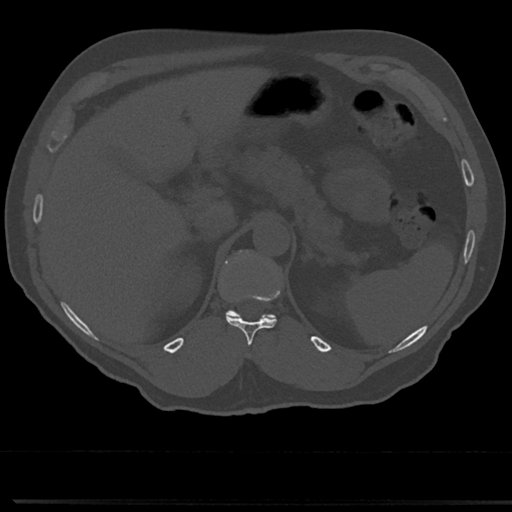
CT including the spine, one axial slice; slice 182 of 817 in the series (ordered by position); reconstruction kernel Br40s/3; 120 kVp; bone window (W 1800 / L 400 HU); 0.5 mm slice thickness; 512 × 512 image matrix, field of view 355 × 355 mm. Patient: male, 61 years. From the clinical record (not read from this slice): primary cancer: prostate.
Outlined on this slice (semi-automatically segmented with operator editing):
- T11 vertebra: box from (x=226, y=317) to (x=277, y=347) px
- T12 vertebra: (x=223, y=250)–(x=276, y=320)